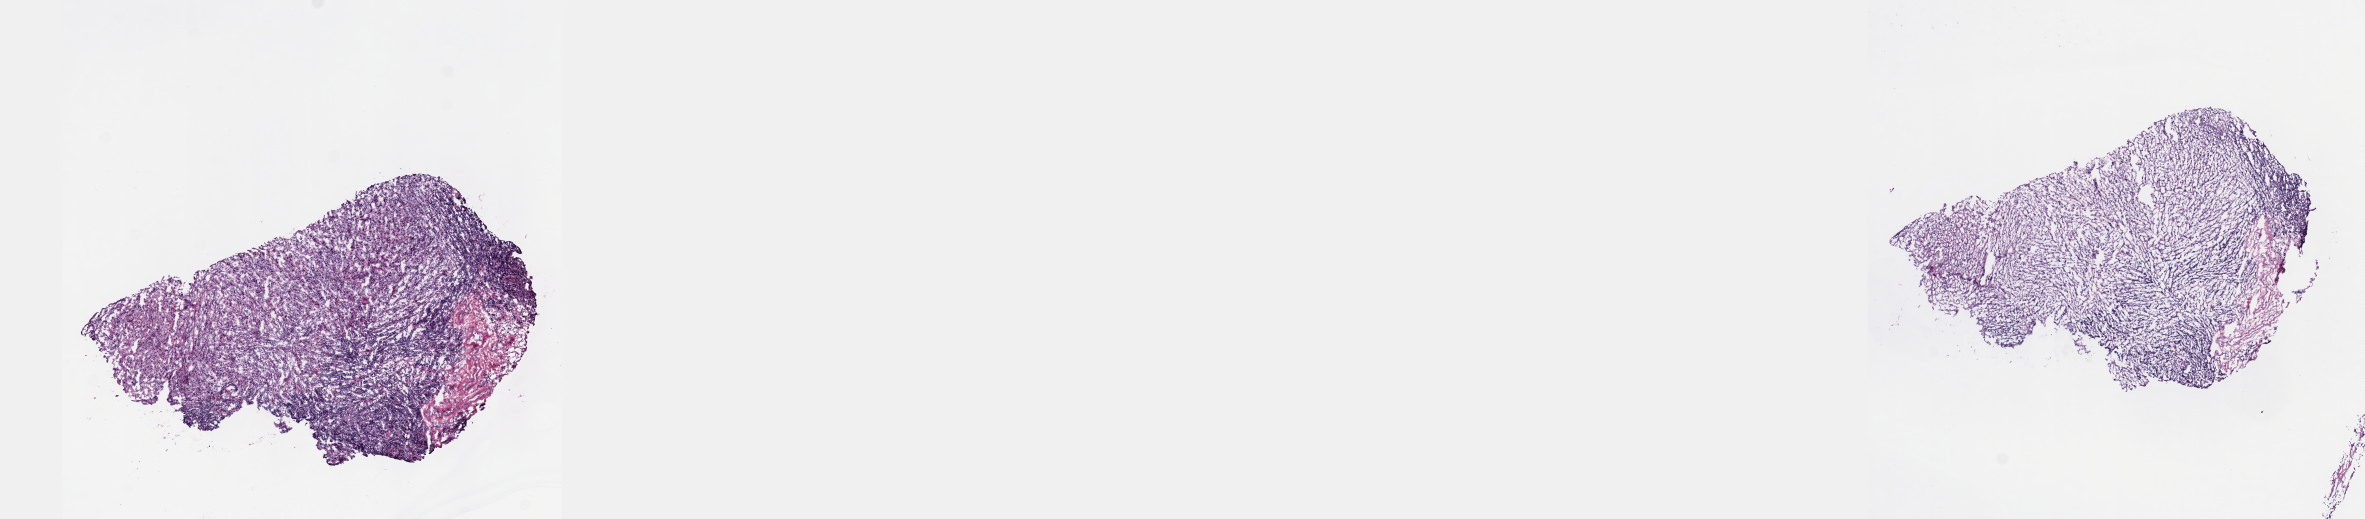
Whole-slide histology image, H&E — shown as a low-resolution overview of the whole scanned area (about 19.1 x 4.2 mm); frozen section from the top of the tissue portion; primary tumour sample from the mesothelium. Male patient; age at initial diagnosis 66 years. Composition of this section per pathologist review: tumour cells 100%, tumour nuclei 85%, normal cells 0%, stromal cells 0%, necrosis 0%. Inflammatory infiltration, as recorded: lymphocyte infiltration 0%, monocyte infiltration 0%, neutrophil infiltration 0%.
• diagnosis: Mesothelioma, malignant (pleura, NOS)
• AJCC pathologic stage: IV (7th edition)